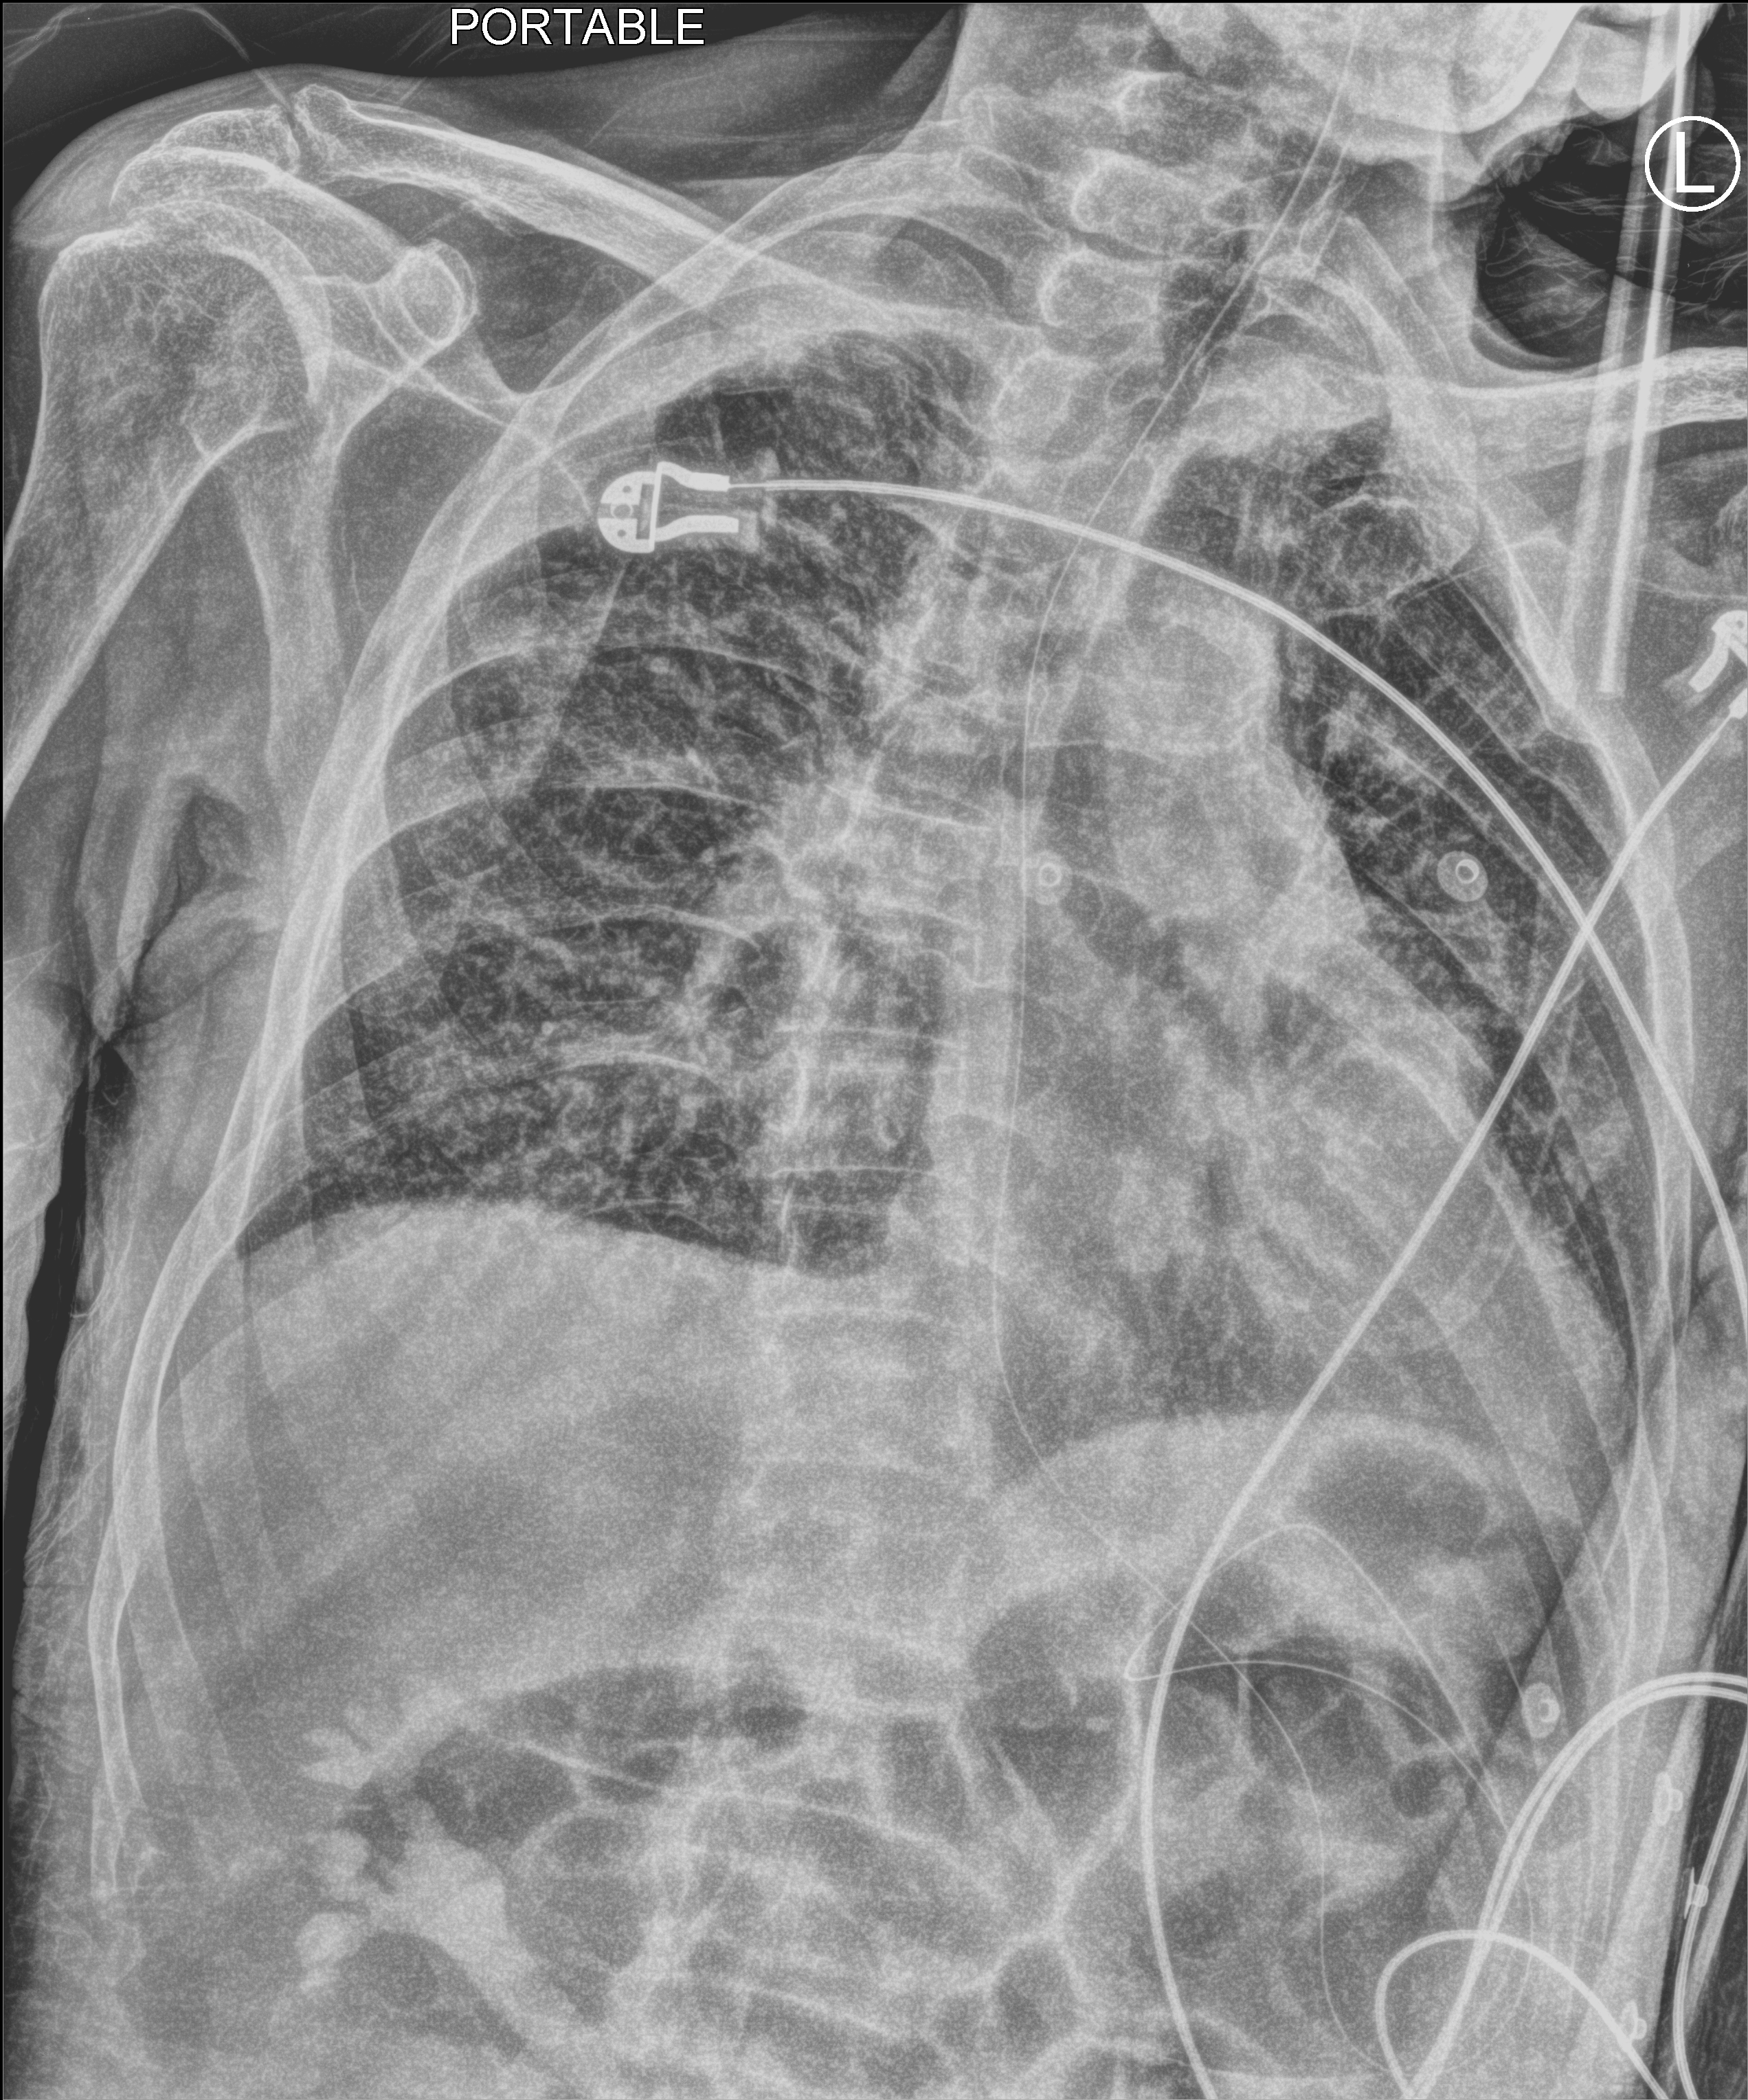
Bedside chest radiograph (computed radiography). Patient hospitalised with COVID-19; male, aged 75–90 years.
From the hospital-stay record, not from the radiograph (when in the stay this image was taken is not recorded): mechanically ventilated during this hospital stay: no; other chronic lung disease (admission record): no; admitted to intensive care during this hospital stay: no.